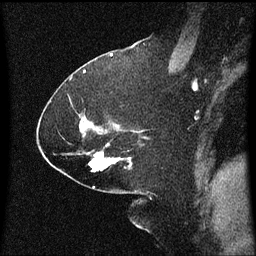
Breast MRI (dynamic contrast-enhanced), one sagittal slice. Position 35 of 60 along the scan axis. Dynamic contrast-enhanced series, image 2 of 3 at this slice position (ordered by acquisition). 1.5 T. TE 4.2 ms, TR 8 ms. 2.1 mm slice thickness. 256 × 256 image matrix, field of view 200 × 200 mm. Female patient, age 59 years.
Outlined on this slice (semi-automatic segmentation, software-assisted and operator-edited):
- analysis volume of interest (the breast-tissue region the enhancement analysis was run in; not a lesion): bounding box <84,144,133,173> (left, top, right, bottom; pixels)
- tumour enhancement mask (voxels above the 70 % enhancement threshold inside the analysis volume of interest): <90,152,121,173>